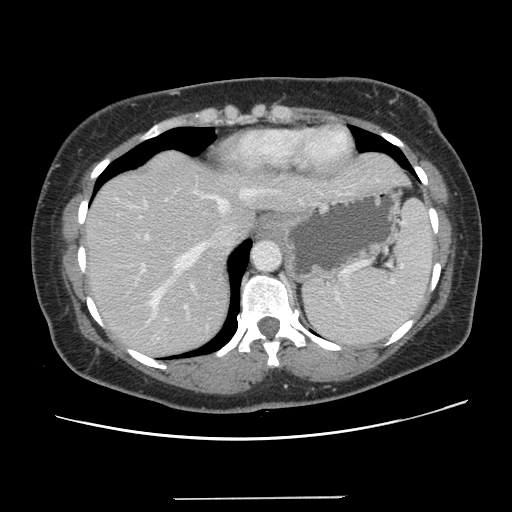
Contrast-enhanced abdominal CT, one axial slice. Position 107 of 141 along the scan axis. 120 kVp. Soft-tissue window (W 400 / L 40 HU). 2.5 mm slice thickness. 512 × 512 image matrix, field of view 366 × 366 mm. Female patient, age 53 years. Case-level facts recorded for this patient, not image findings: diagnosis: colorectal cancer liver metastases, imaged before liver resection; multiple liver metastases: no; largest metastasis: 14.5 cm; disease in both lobes: yes.
Outlined on this slice (outlined manually by an expert reader):
- hepatic veins: bounding box [x1, y1, x2, y2] px = [113, 186, 280, 317]
- liver: [85, 150, 408, 358]
- planned liver remnant (the part of the liver to remain after resection): [85, 208, 257, 358]
- portal vein (with intrahepatic branches): [139, 198, 189, 322]